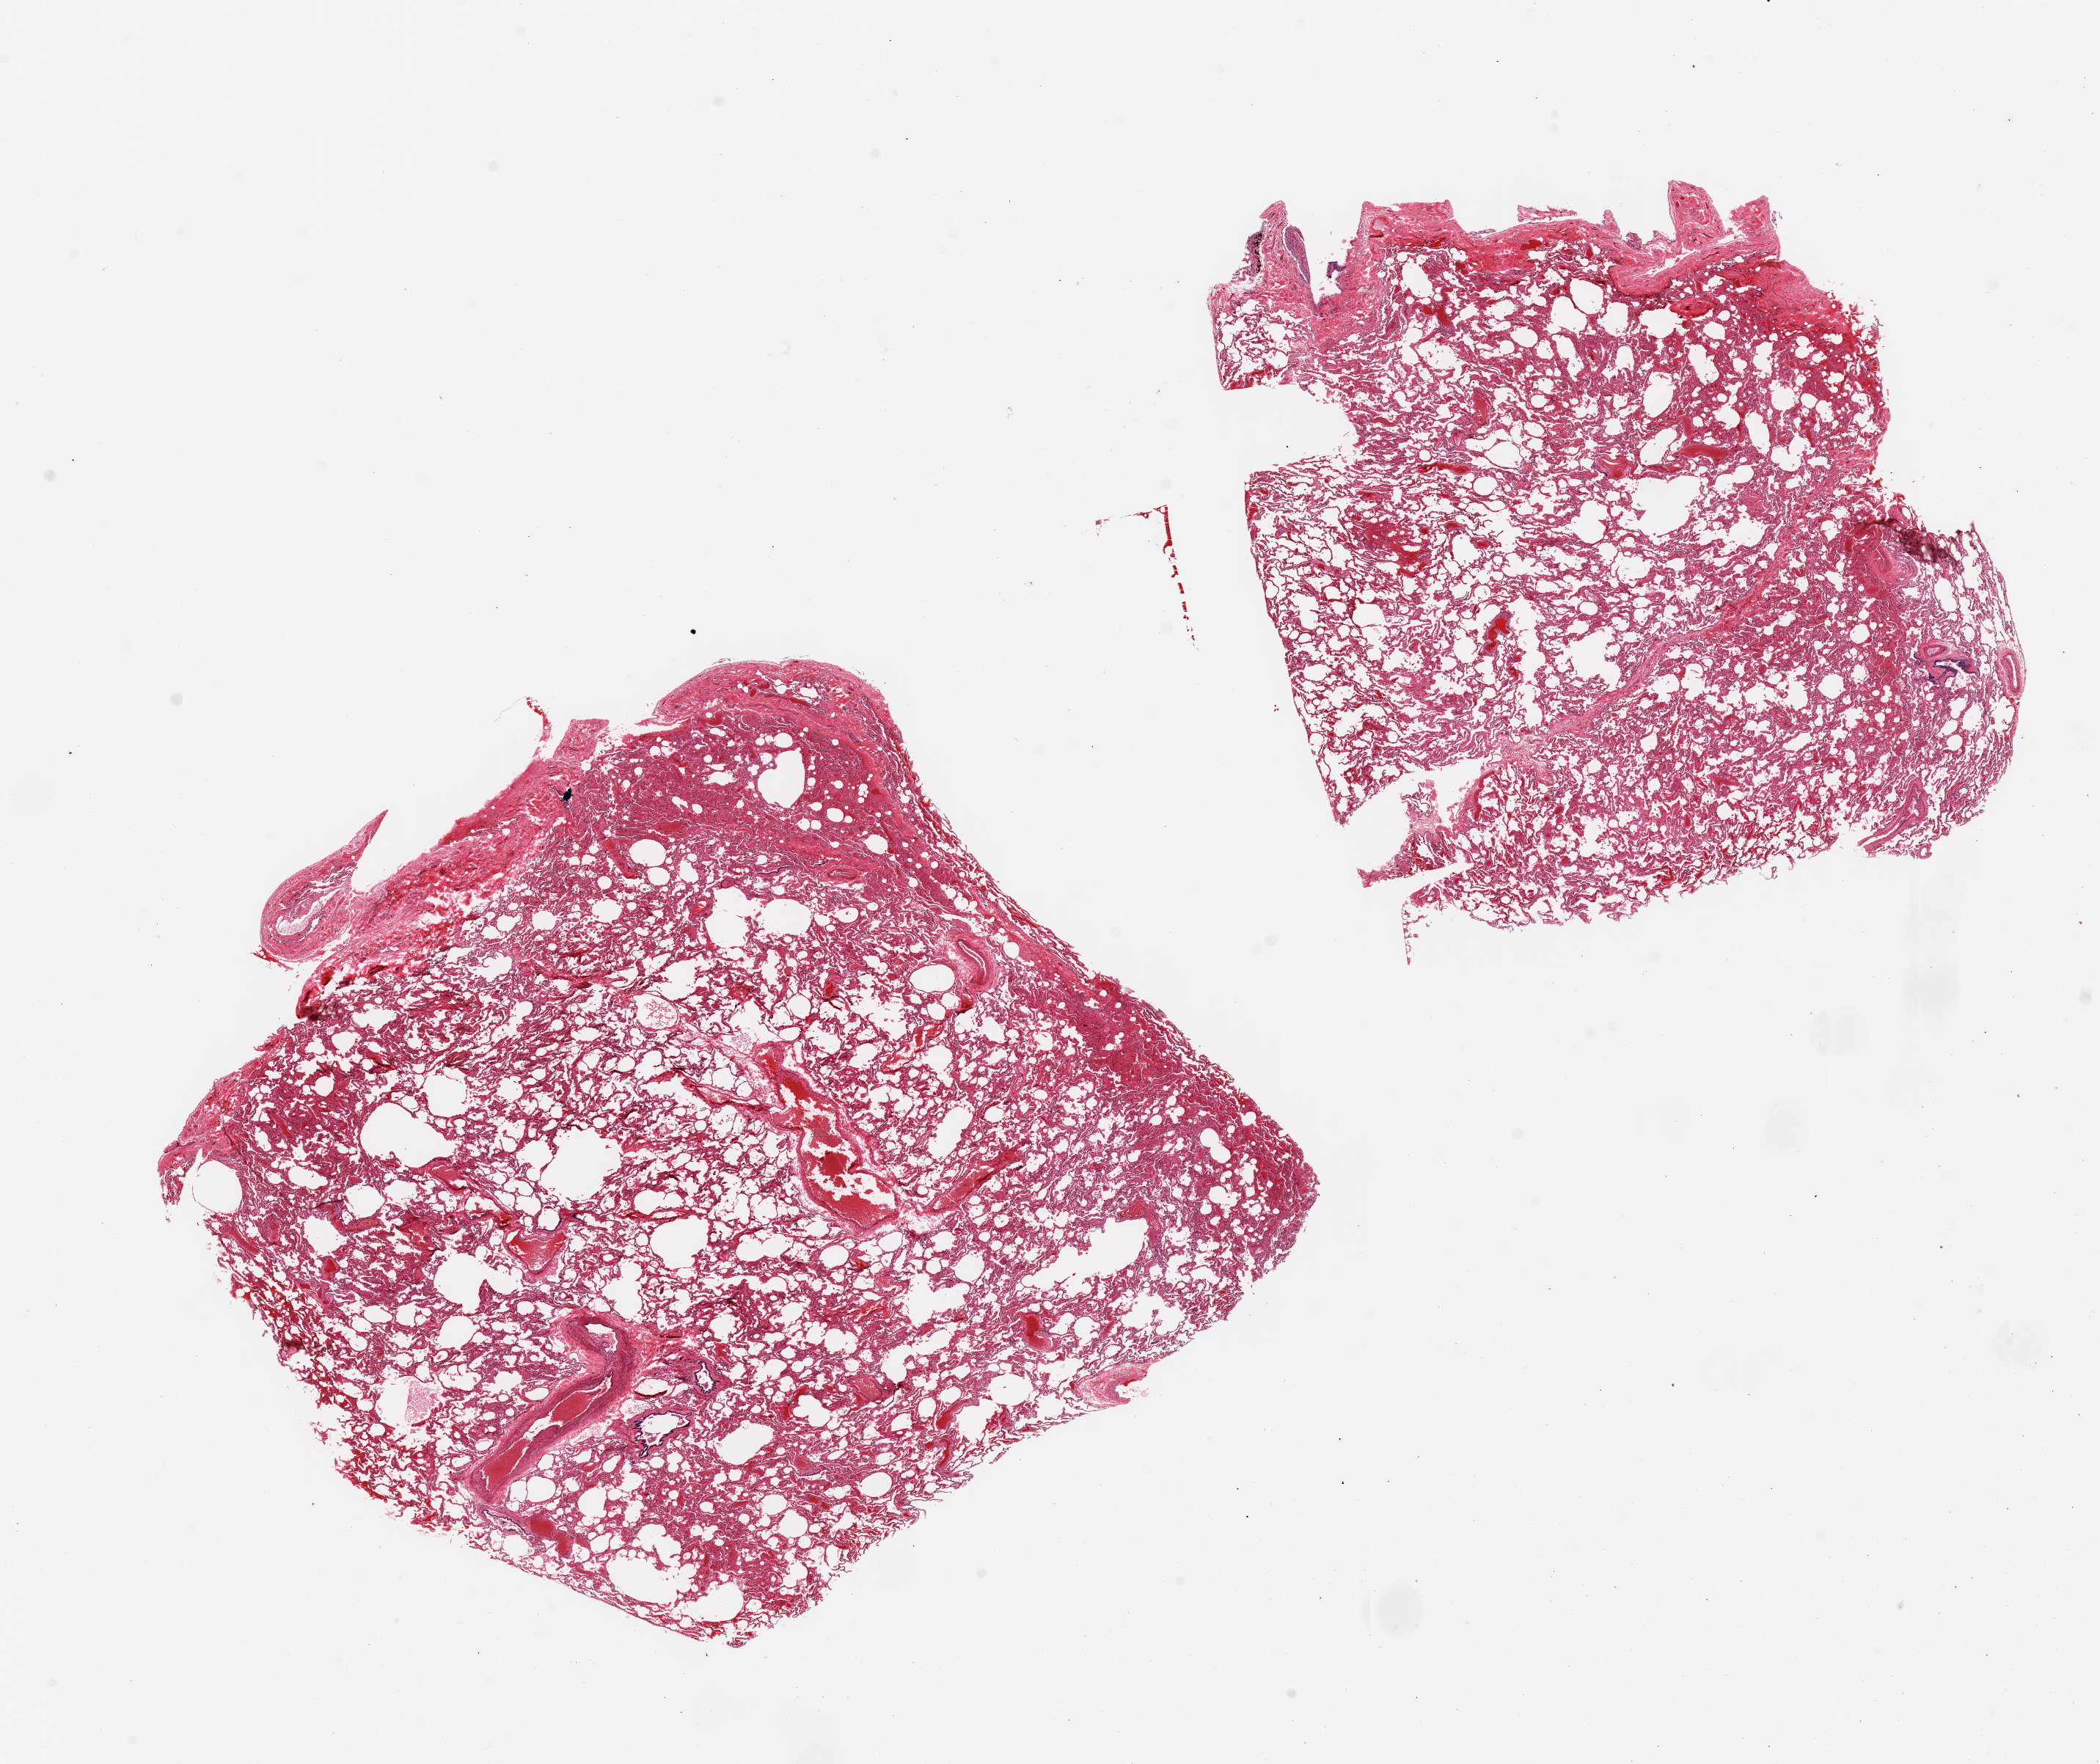
Digitized hematoxylin and eosin (H&E)-stained section, brightfield — low-resolution overview of the scanned area, about 22.6 x 19.0 mm, PAXgene-fixed, paraffin-embedded tissue, sampled site (target tissue): lung, donor tissue sample. Male donor.
• reviewer comment on this tissue sample: 2 pieces, mild congestion